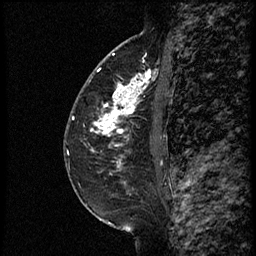
Breast MRI (dynamic contrast-enhanced), one sagittal slice; position 36 of 60 along the scan axis; dynamic contrast-enhanced study with each time point stored as its own series, time point 2 of 3 at this slice position (early post-contrast, ordered by acquisition time); 1.5 T; TE 4.2 ms, TR 18.9 ms; 256 × 256 image matrix, field of view 200 × 200 mm. Female patient. From the clinical record (not read from this slice): setting: breast cancer imaged before/during neoadjuvant chemotherapy; receptor status: HER2-positive.
Structures marked on this image (semi-automatic segmentation, software-assisted and operator-edited):
- analysis volume of interest (the breast-tissue region the enhancement analysis was run in; not a lesion): bounding box [x1, y1, x2, y2] px = [83, 64, 161, 147]
- tumour enhancement mask (voxels above the 100 % enhancement threshold inside the analysis volume of interest): [93, 75, 150, 146]